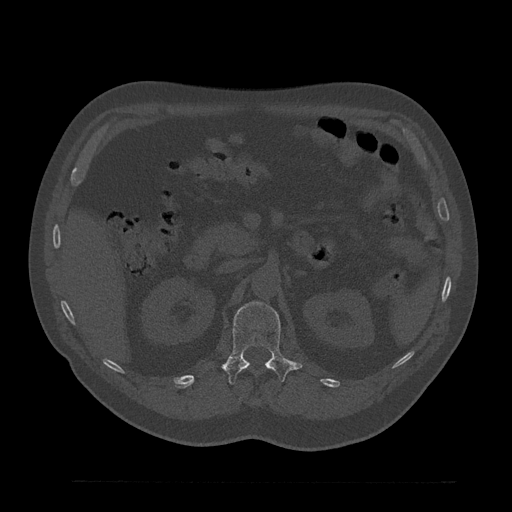
CT including the spine, one axial slice. Position 177 of 797 along the scan axis. Reconstruction kernel Br40s/3. Bone window (W 1800 / L 400 HU). 0.5 mm slice thickness. 512 × 512 image matrix, field of view 430 × 430 mm. Patient: male, 61 years. From the clinical record (not read from this slice): primary cancer: prostate.
Annotated regions visible in this slice (semi-automatically segmented with operator editing):
- L1 vertebra: box from (x=223, y=301) to (x=302, y=385) px